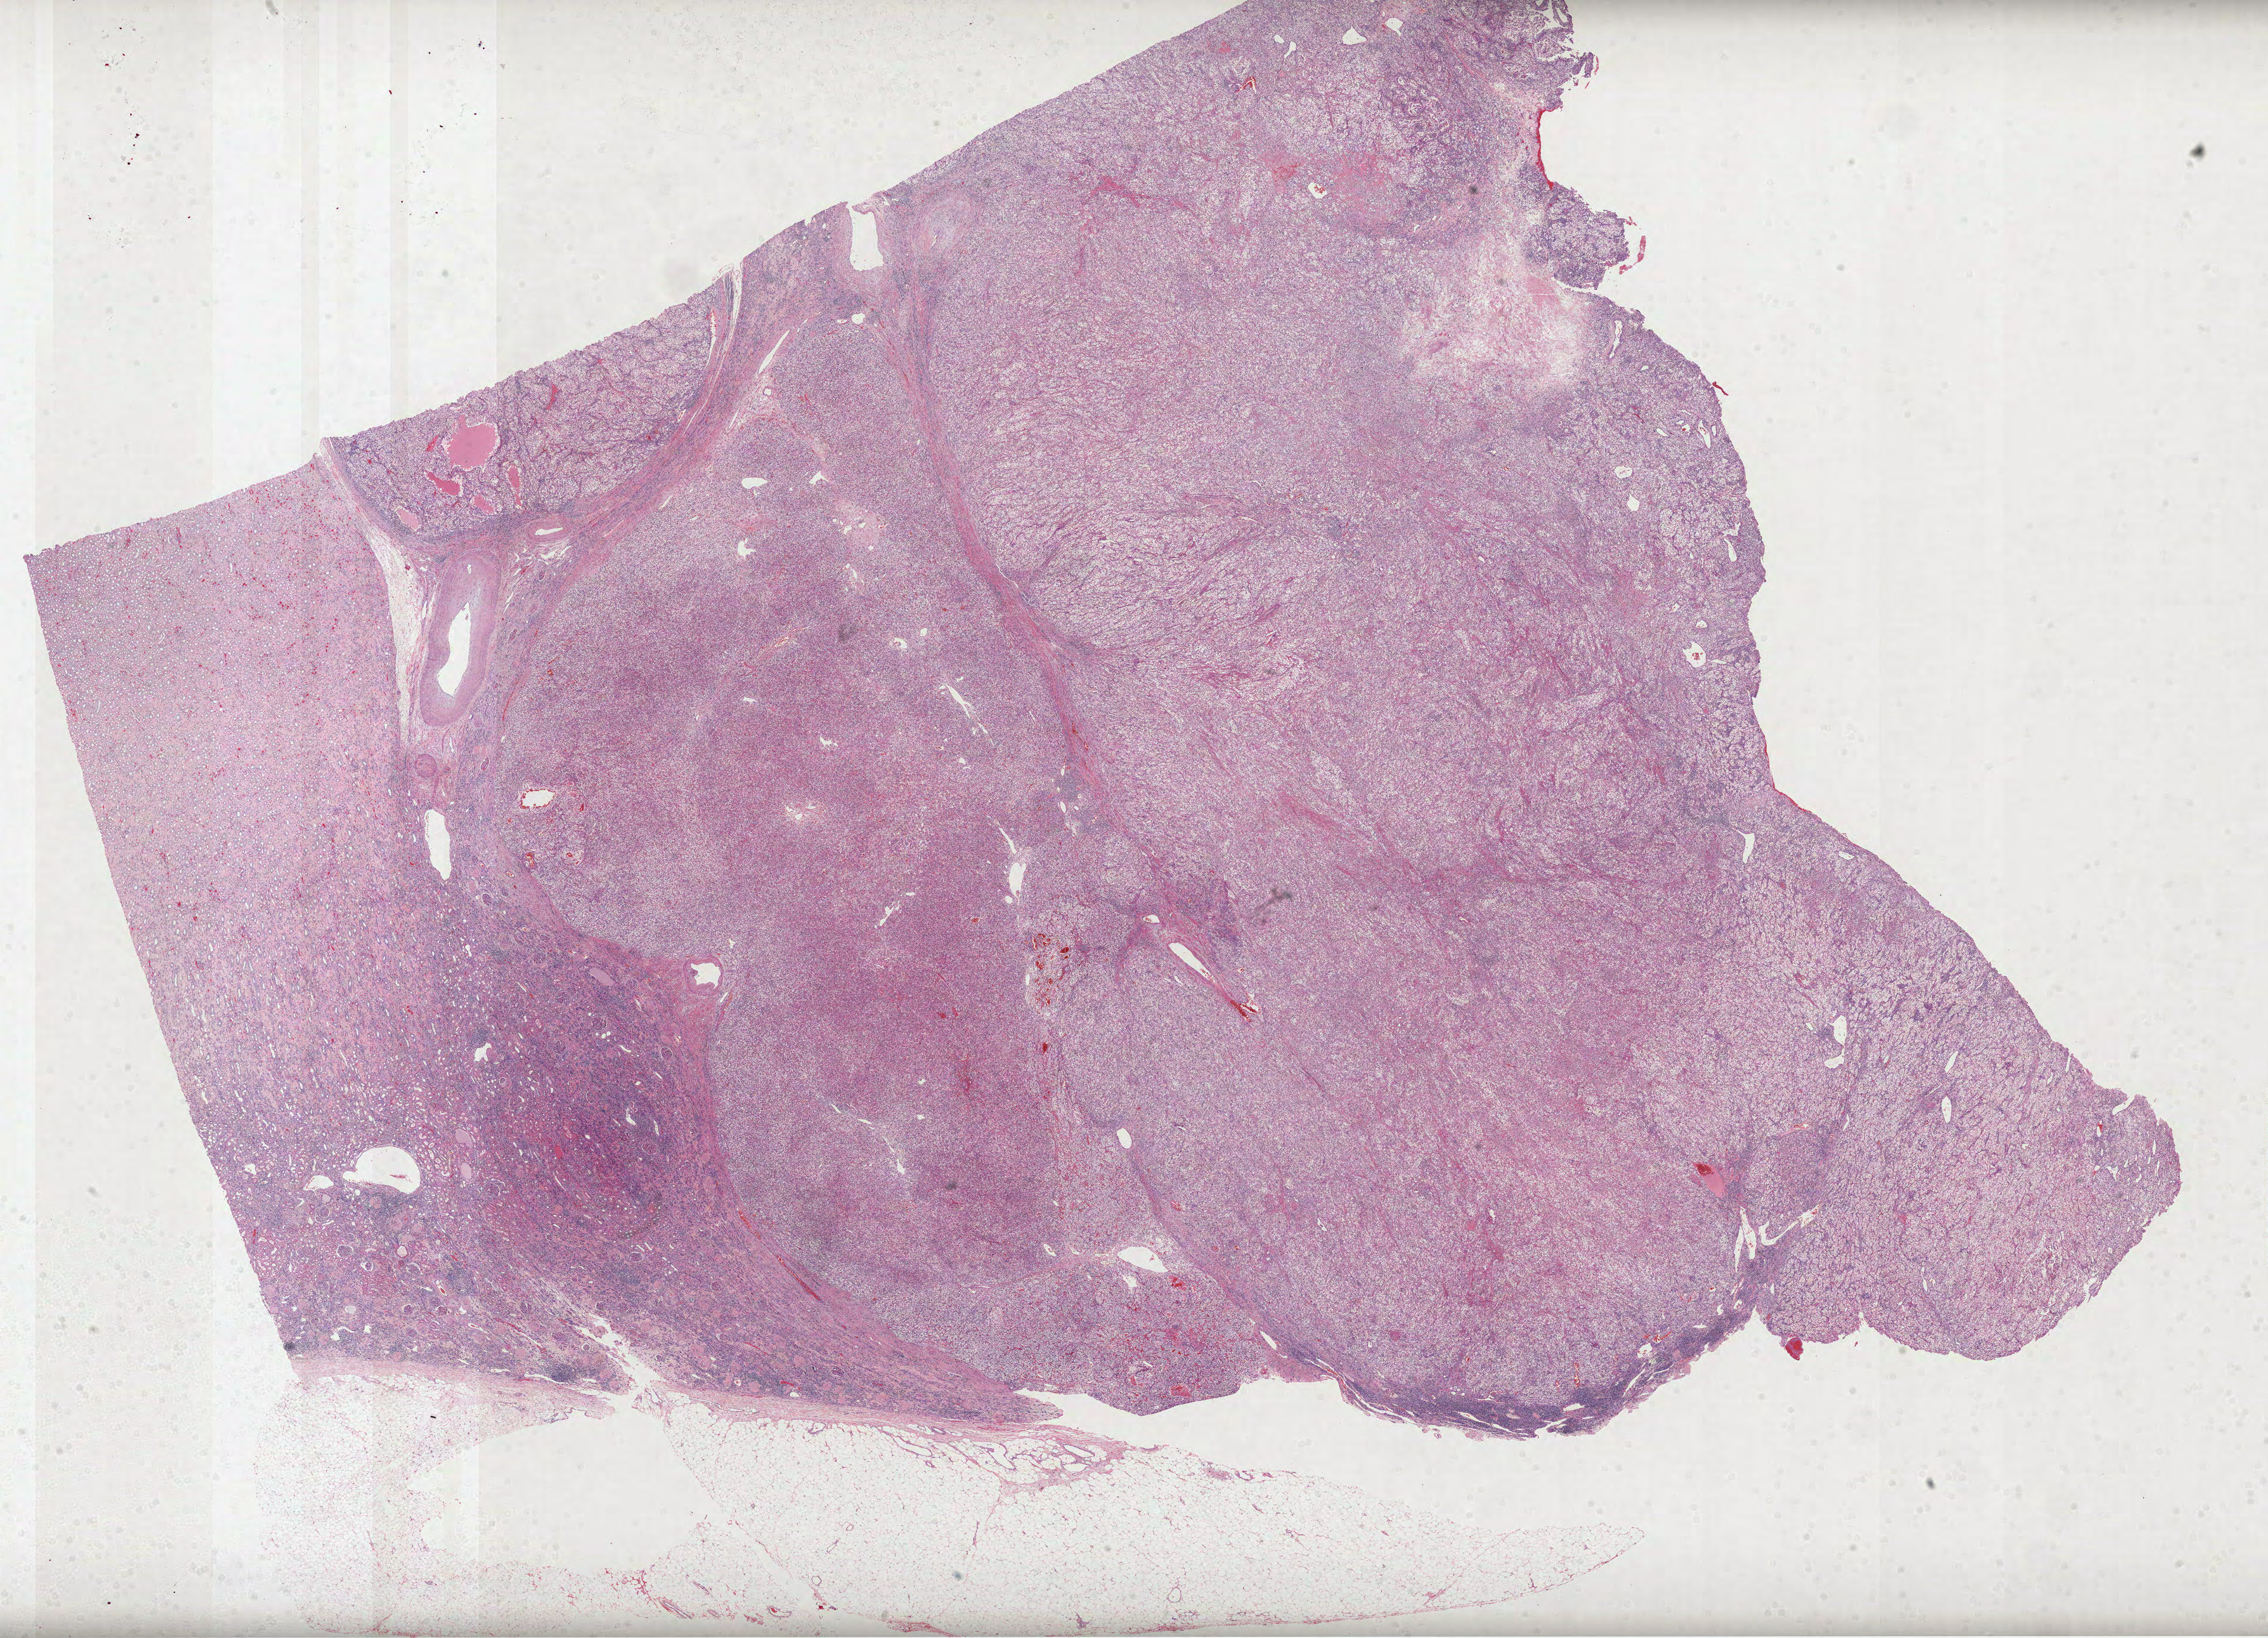
Digitized H&E-stained tissue section (whole slide), a low-resolution overview of the entire scanned area, about 30.9 x 22.3 mm (acquisition: 40x scan); formalin-fixed paraffin-embedded (FFPE) diagnostic section; kidney, primary tumour sample. Patient: female, age at initial diagnosis 79 years. Histologic grade: G2 (moderately differentiated).
• pathologic diagnosis: Clear cell adenocarcinoma, NOS
• AJCC pathologic stage: III
• laterality: right